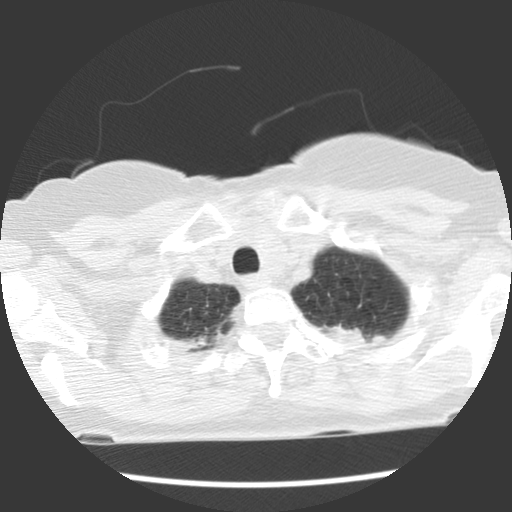
Low-dose screening chest CT, one axial slice; position 105 of 120 along the scan axis; reconstruction kernel STANDARD; 140 kVp; lung window (W 1500 / L -600 HU); 2.5 mm slice thickness; 512 × 512 image matrix.
Outlined on this slice (outlined manually by an expert reader):
- lesion 1 (tumor, upper lobe of left lung): bounding box <329,325,388,344> (left, top, right, bottom; pixels)